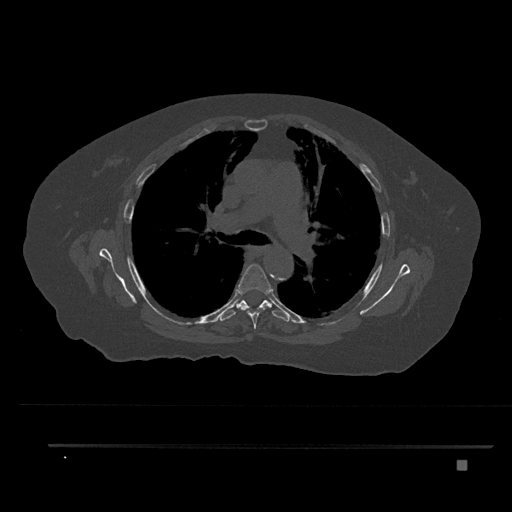
CT including the spine, one axial slice. Position 550 of 797 along the scan axis. Reconstruction kernel Br40s/3. Bone window (W 1800 / L 400 HU). 0.5 mm slice thickness. 512 × 512 image matrix, field of view 437 × 437 mm. Patient: female, 76 years. Case-level facts recorded for this patient, not image findings: primary cancer: lung; vertebrae with lytic lesions (as recorded): T11, L3.
Annotated regions visible in this slice (semi-automatically segmented with operator editing):
- T5 vertebra: bounding box [x1, y1, x2, y2] px = [238, 264, 271, 329]
- T6 vertebra: [219, 300, 290, 322]